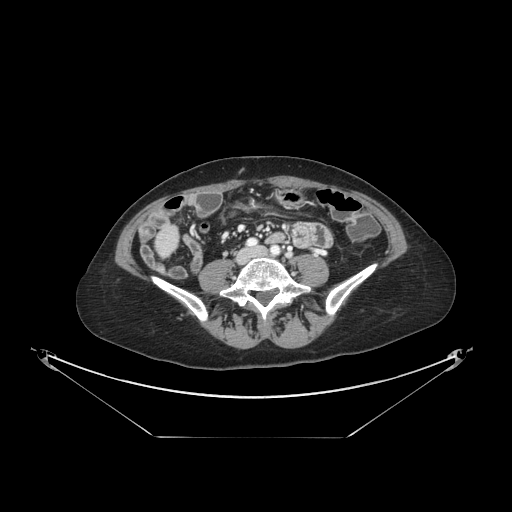
Contrast-enhanced abdominal CT, one axial slice. Reconstruction kernel STANDARD. Intravenous contrast given. Soft-tissue window (W 400 / L 40 HU). 512 × 512 image matrix, field of view 500 × 500 mm. Female patient, age 73 years. Case-level facts recorded for this patient, not image findings: diagnosis: colorectal cancer liver metastases, imaged before liver resection; multiple liver metastases: no.
Annotated regions visible in this slice (expert manual segmentation):
- liver: box from (x=157, y=230) to (x=177, y=255) px